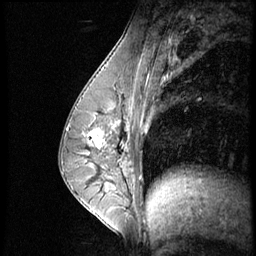
Breast MRI (dynamic contrast-enhanced), one sagittal slice; slice 28 of 56 in the series (ordered by position); dynamic contrast-enhanced series, image 2 of 4 at this slice position (ordered by acquisition); 1.5 T; TE 4.2 ms, TR 8.9 ms; 2.5 mm slice thickness; 256 × 256 image matrix. Patient: female, 35 years. Case-level facts recorded for this patient, not image findings: setting: breast cancer imaged before/during neoadjuvant chemotherapy; receptor status: HER2-positive.
Structures marked on this image (semi-automatic segmentation, software-assisted and operator-edited):
- analysis volume of interest (the breast-tissue region the enhancement analysis was run in; not a lesion): box from (x=73, y=111) to (x=131, y=164) px
- tumour enhancement mask (voxels above the 140 % enhancement threshold inside the analysis volume of interest): (x=78, y=128)–(x=104, y=164)